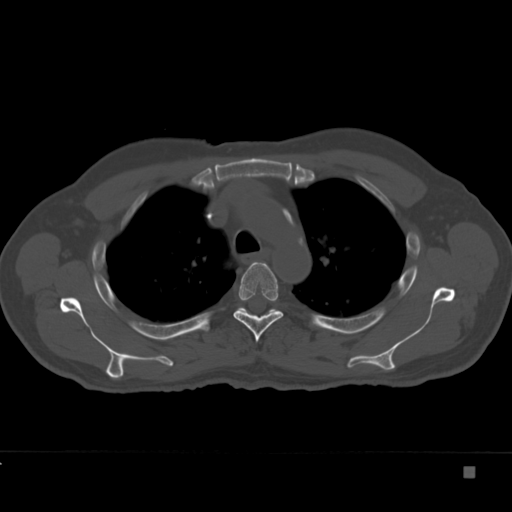
CT including the spine, one axial slice. Slice 270 of 332 in the series (ordered by position). Bone window (W 1800 / L 400 HU). 1.5 mm slice thickness. 512 × 512 image matrix, field of view 389 × 389 mm. Male patient, age 72 years. Case-level facts recorded for this patient, not image findings: primary cancer: skeletal.
Annotated regions visible in this slice (semi-automatically segmented with operator editing):
- T4 vertebra: bounding box (x1, y1, x2, y2) in pixels: (233, 262, 283, 342)
- T5 vertebra: (241, 307, 272, 313)